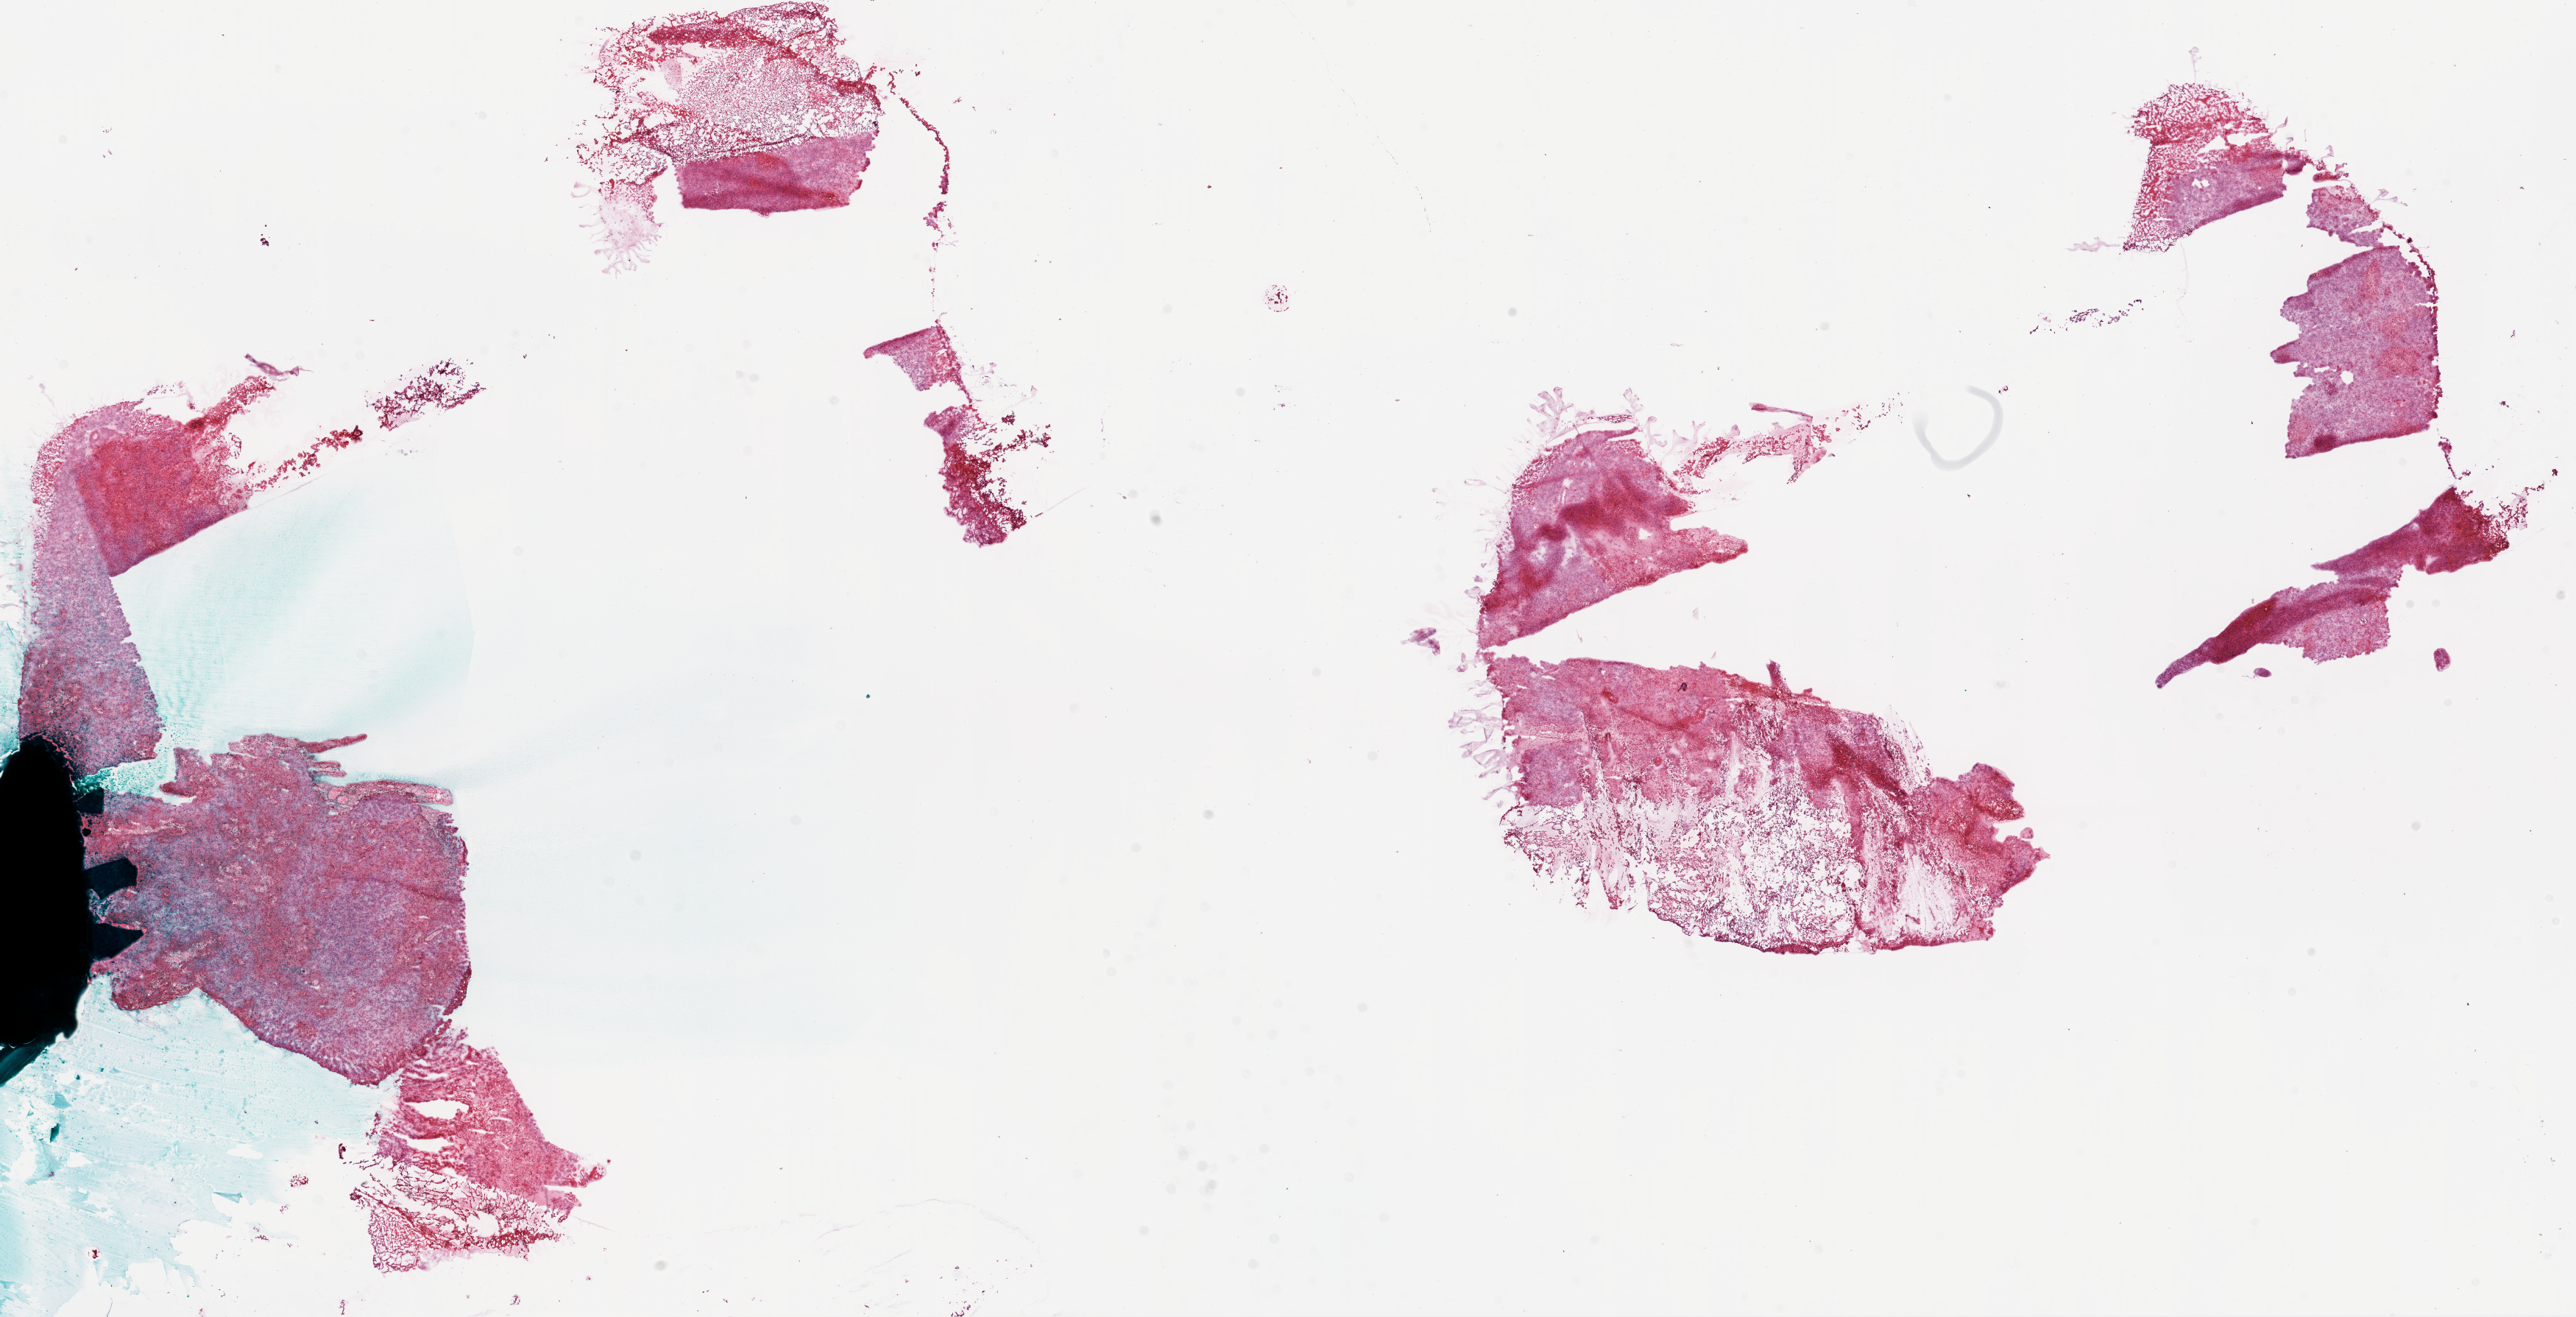
Digitized H&E tissue section (whole slide), low-resolution overview of the scanned area, about 28.1 x 14.4 mm (slide scanned at 20x); frozen section from the bottom of the tissue portion; primary tumour sample from the brain. Patient: female, age at initial diagnosis 50 years. Slide review estimates, as recorded: tumour cells 90%, tumour nuclei 100%, normal cells 0%, stromal cells 0%, necrosis 10%.
Pathologic diagnosis: Glioblastoma.